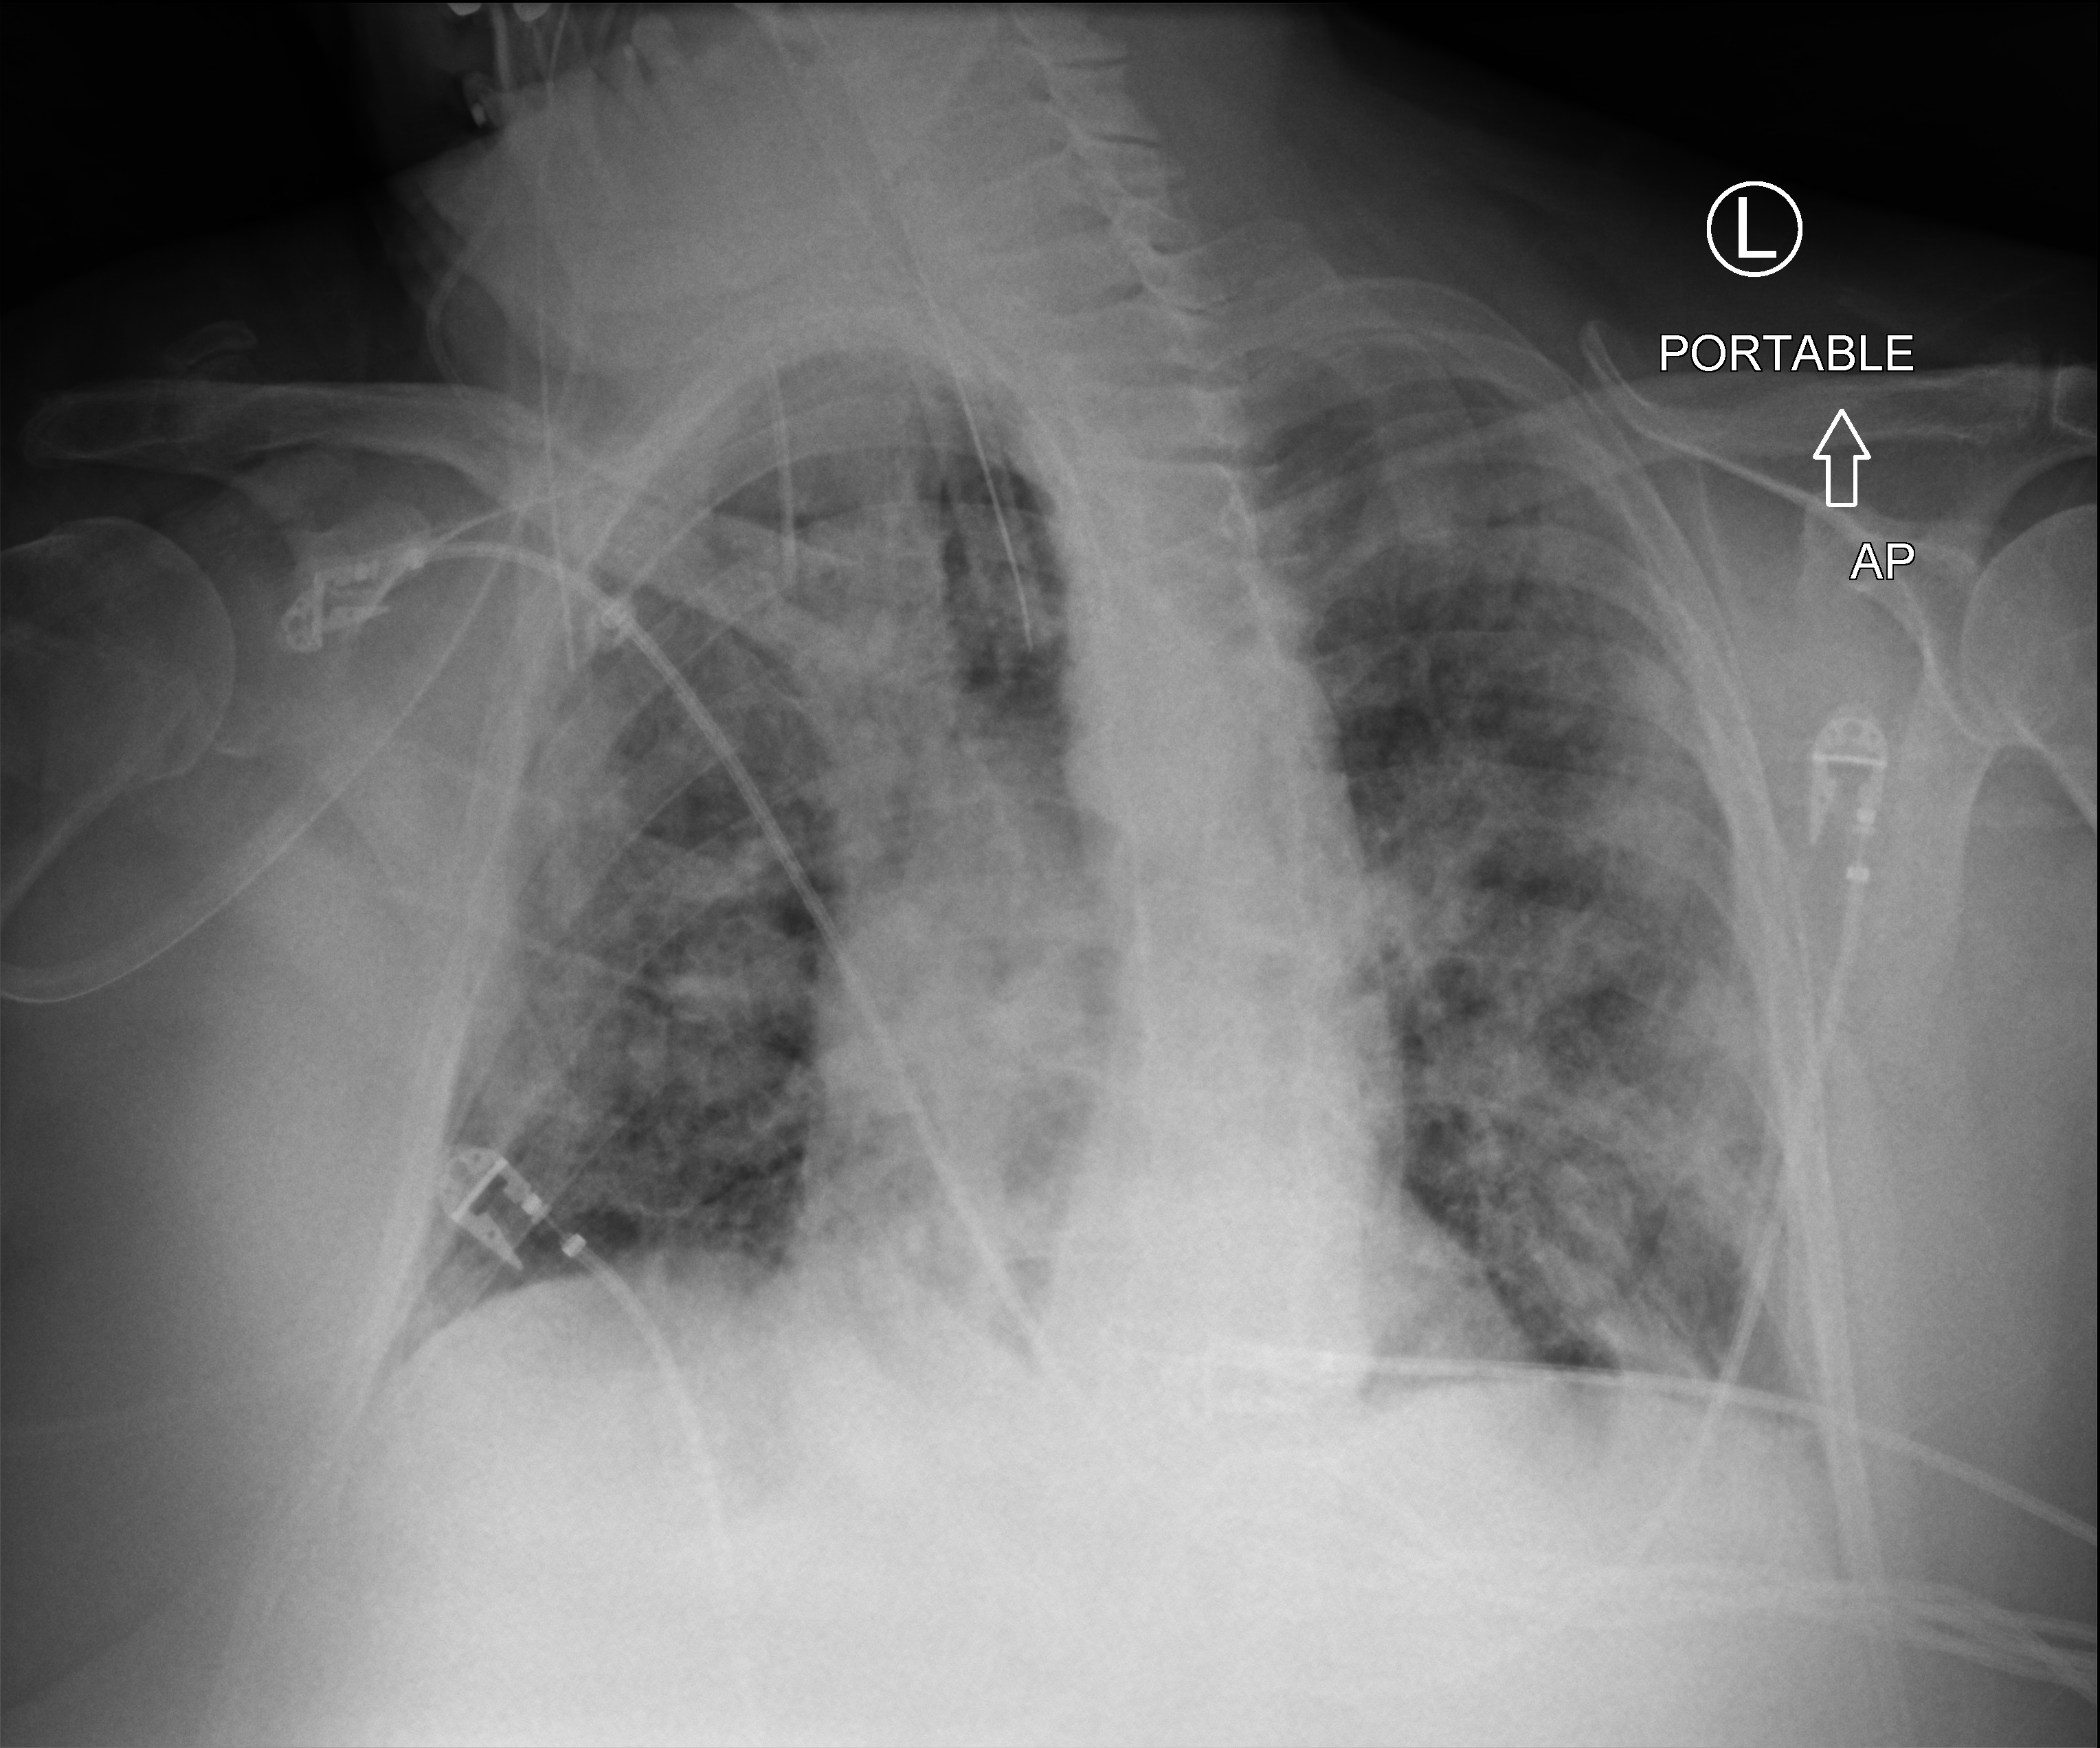
Portable chest radiograph. Patient hospitalised with COVID-19; male, aged 60–74 years.
Admission-level facts for this patient (not findings on this image; timing relative to this image not recorded):
- mechanically ventilated during this hospital stay: yes
- admitted to intensive care during this hospital stay: yes
- COPD (admission record): no